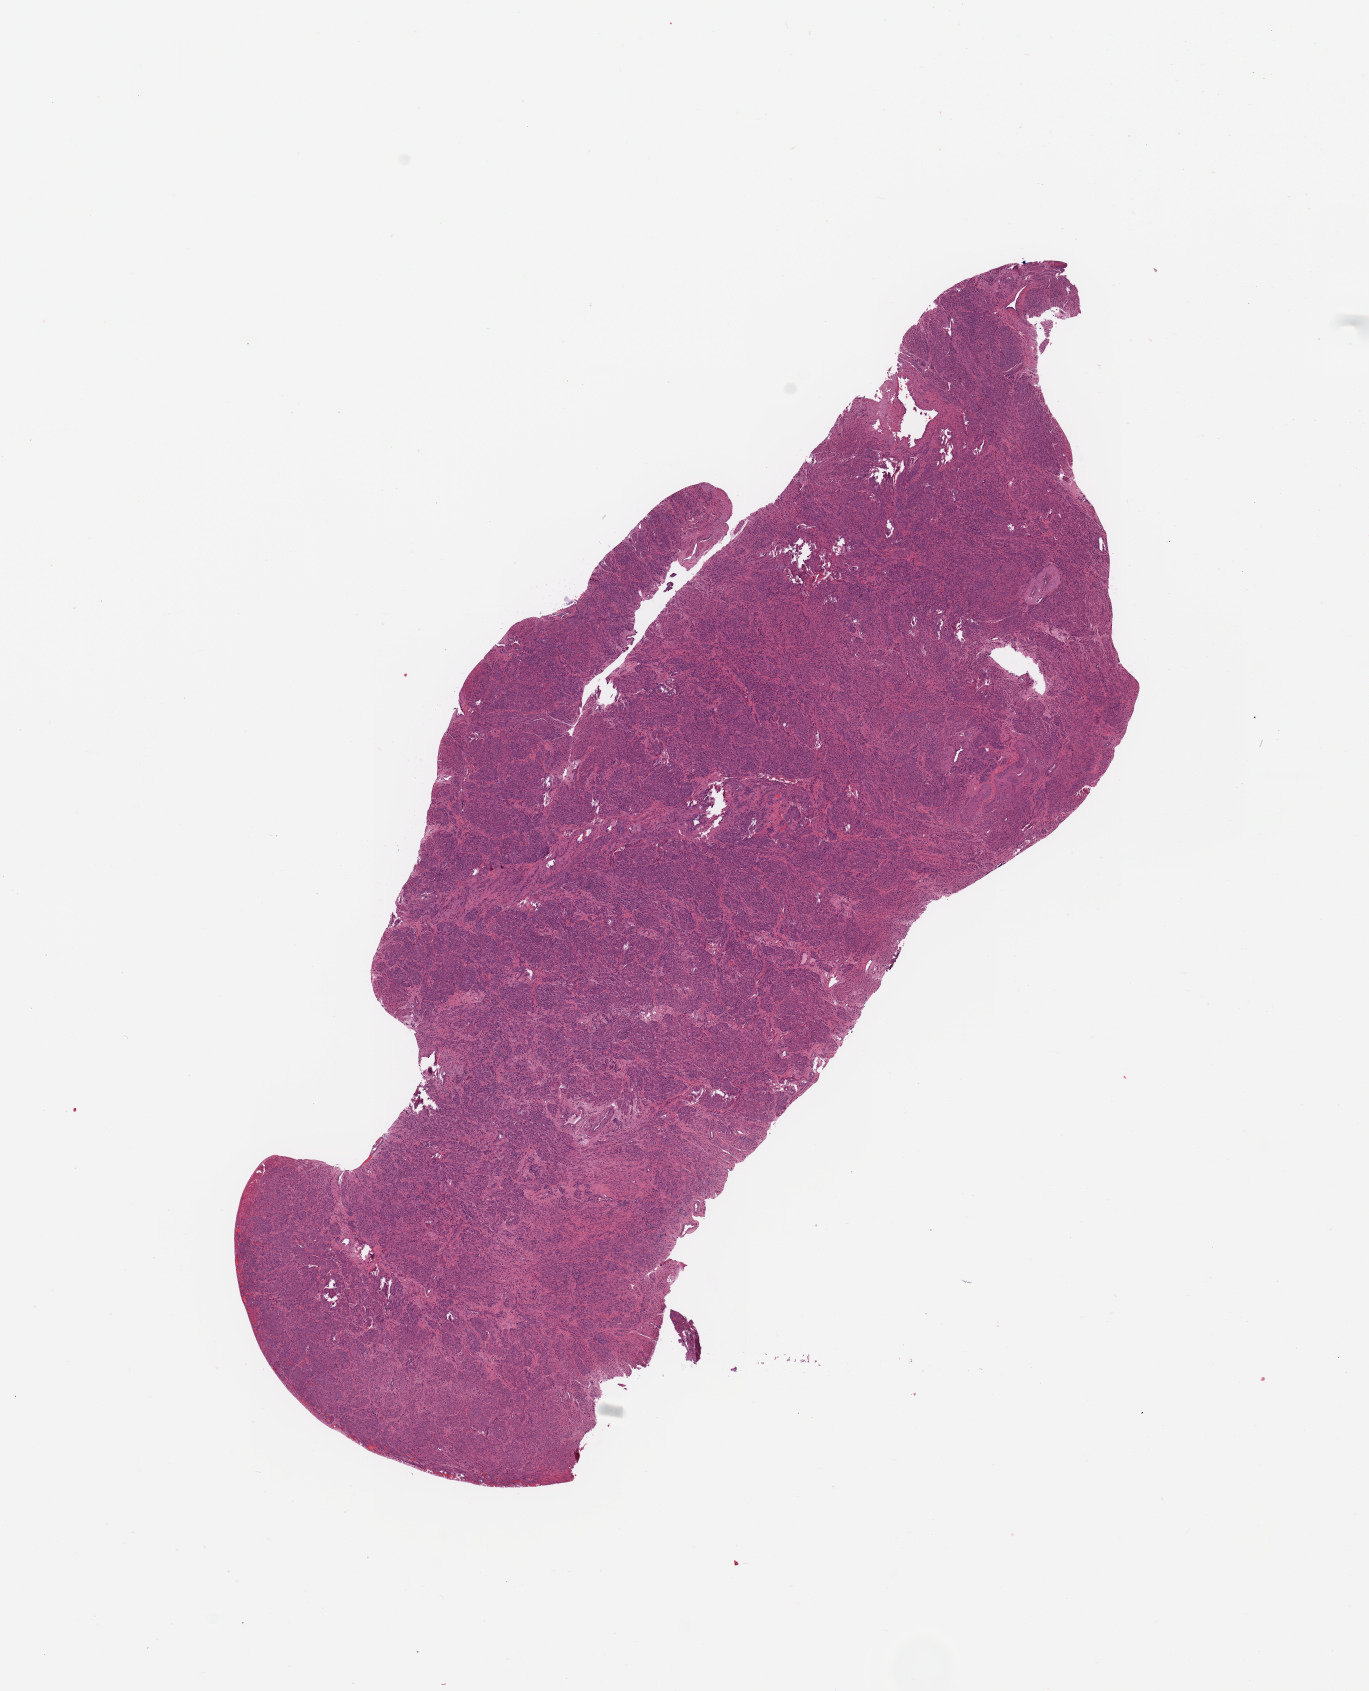
Whole-slide histology image, H&E-stained, a low-resolution overview of the entire scanned area, about 10.8 x 13.4 mm (slide scanned at 20x). Normal (non-tumour) tissue sample, uterus. Female, 55 y/o.
This section: normal (non-tumour) tissue from the same patient. Patient diagnosis: Endometrioid adenocarcinoma, NOS.